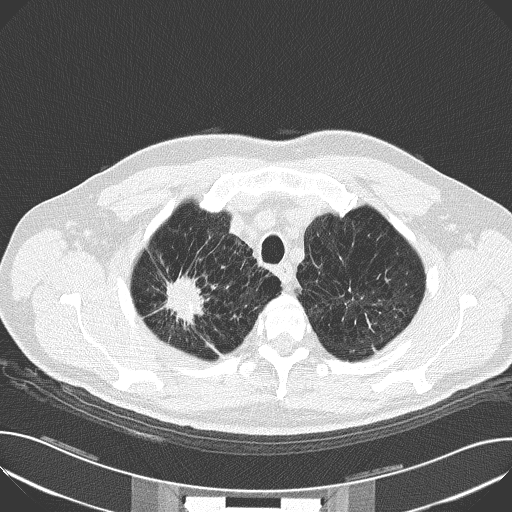
Chest CT (low-dose screening protocol), one axial image. Baseline annual screen. Lung window (W 1500 / L -600 HU). Lung (sharp) reconstruction kernel (B50f). 120 kVp. Slice 23 of 159 in the series. Male, age 59 years at enrolment. Current smoker at enrolment.
- Expert-annotated lung lesion, box from (x=154, y=260) to (x=218, y=329) px.
- The screening reader recorded 4 non-calcified nodules or masses ≥4 mm on this exam; which of them this box marks is not recorded.
- Official screen result: positive, change unspecified: nodule(s) >= 4 mm or enlarging nodule(s), mass(es), or other non-specific abnormalities suspicious for lung cancer.
- Participant outcome: lung cancer diagnosed 44 days after this screen — squamous cell carcinoma, NOS, right upper lobe, moderately differentiated (G2), stage IA (AJCC 6th edition), 30 mm at pathology.